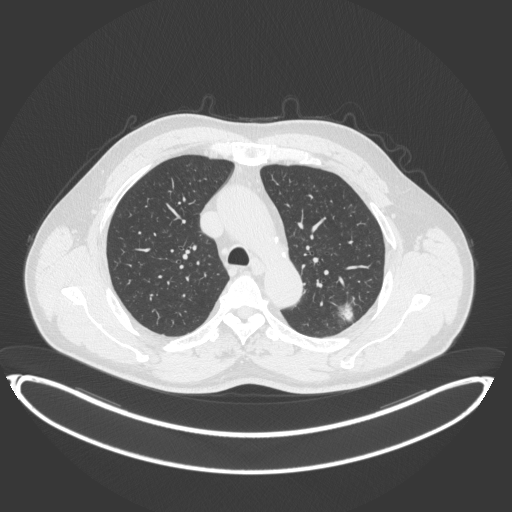
Chest CT, one axial slice; 120 kVp; lung window (W 1500 / L -600 HU); 1 mm slice thickness; 512 × 512 image matrix. Patient: male, 58 years. From the clinical record (not read from this slice): clinical TNM (as recorded): T1c N0 M0.
Structures marked on this image (bounding box drawn by a radiologist):
- lung tumour (recorded histology: adenocarcinoma): bounding box [x1, y1, x2, y2] px = [328, 298, 358, 325]